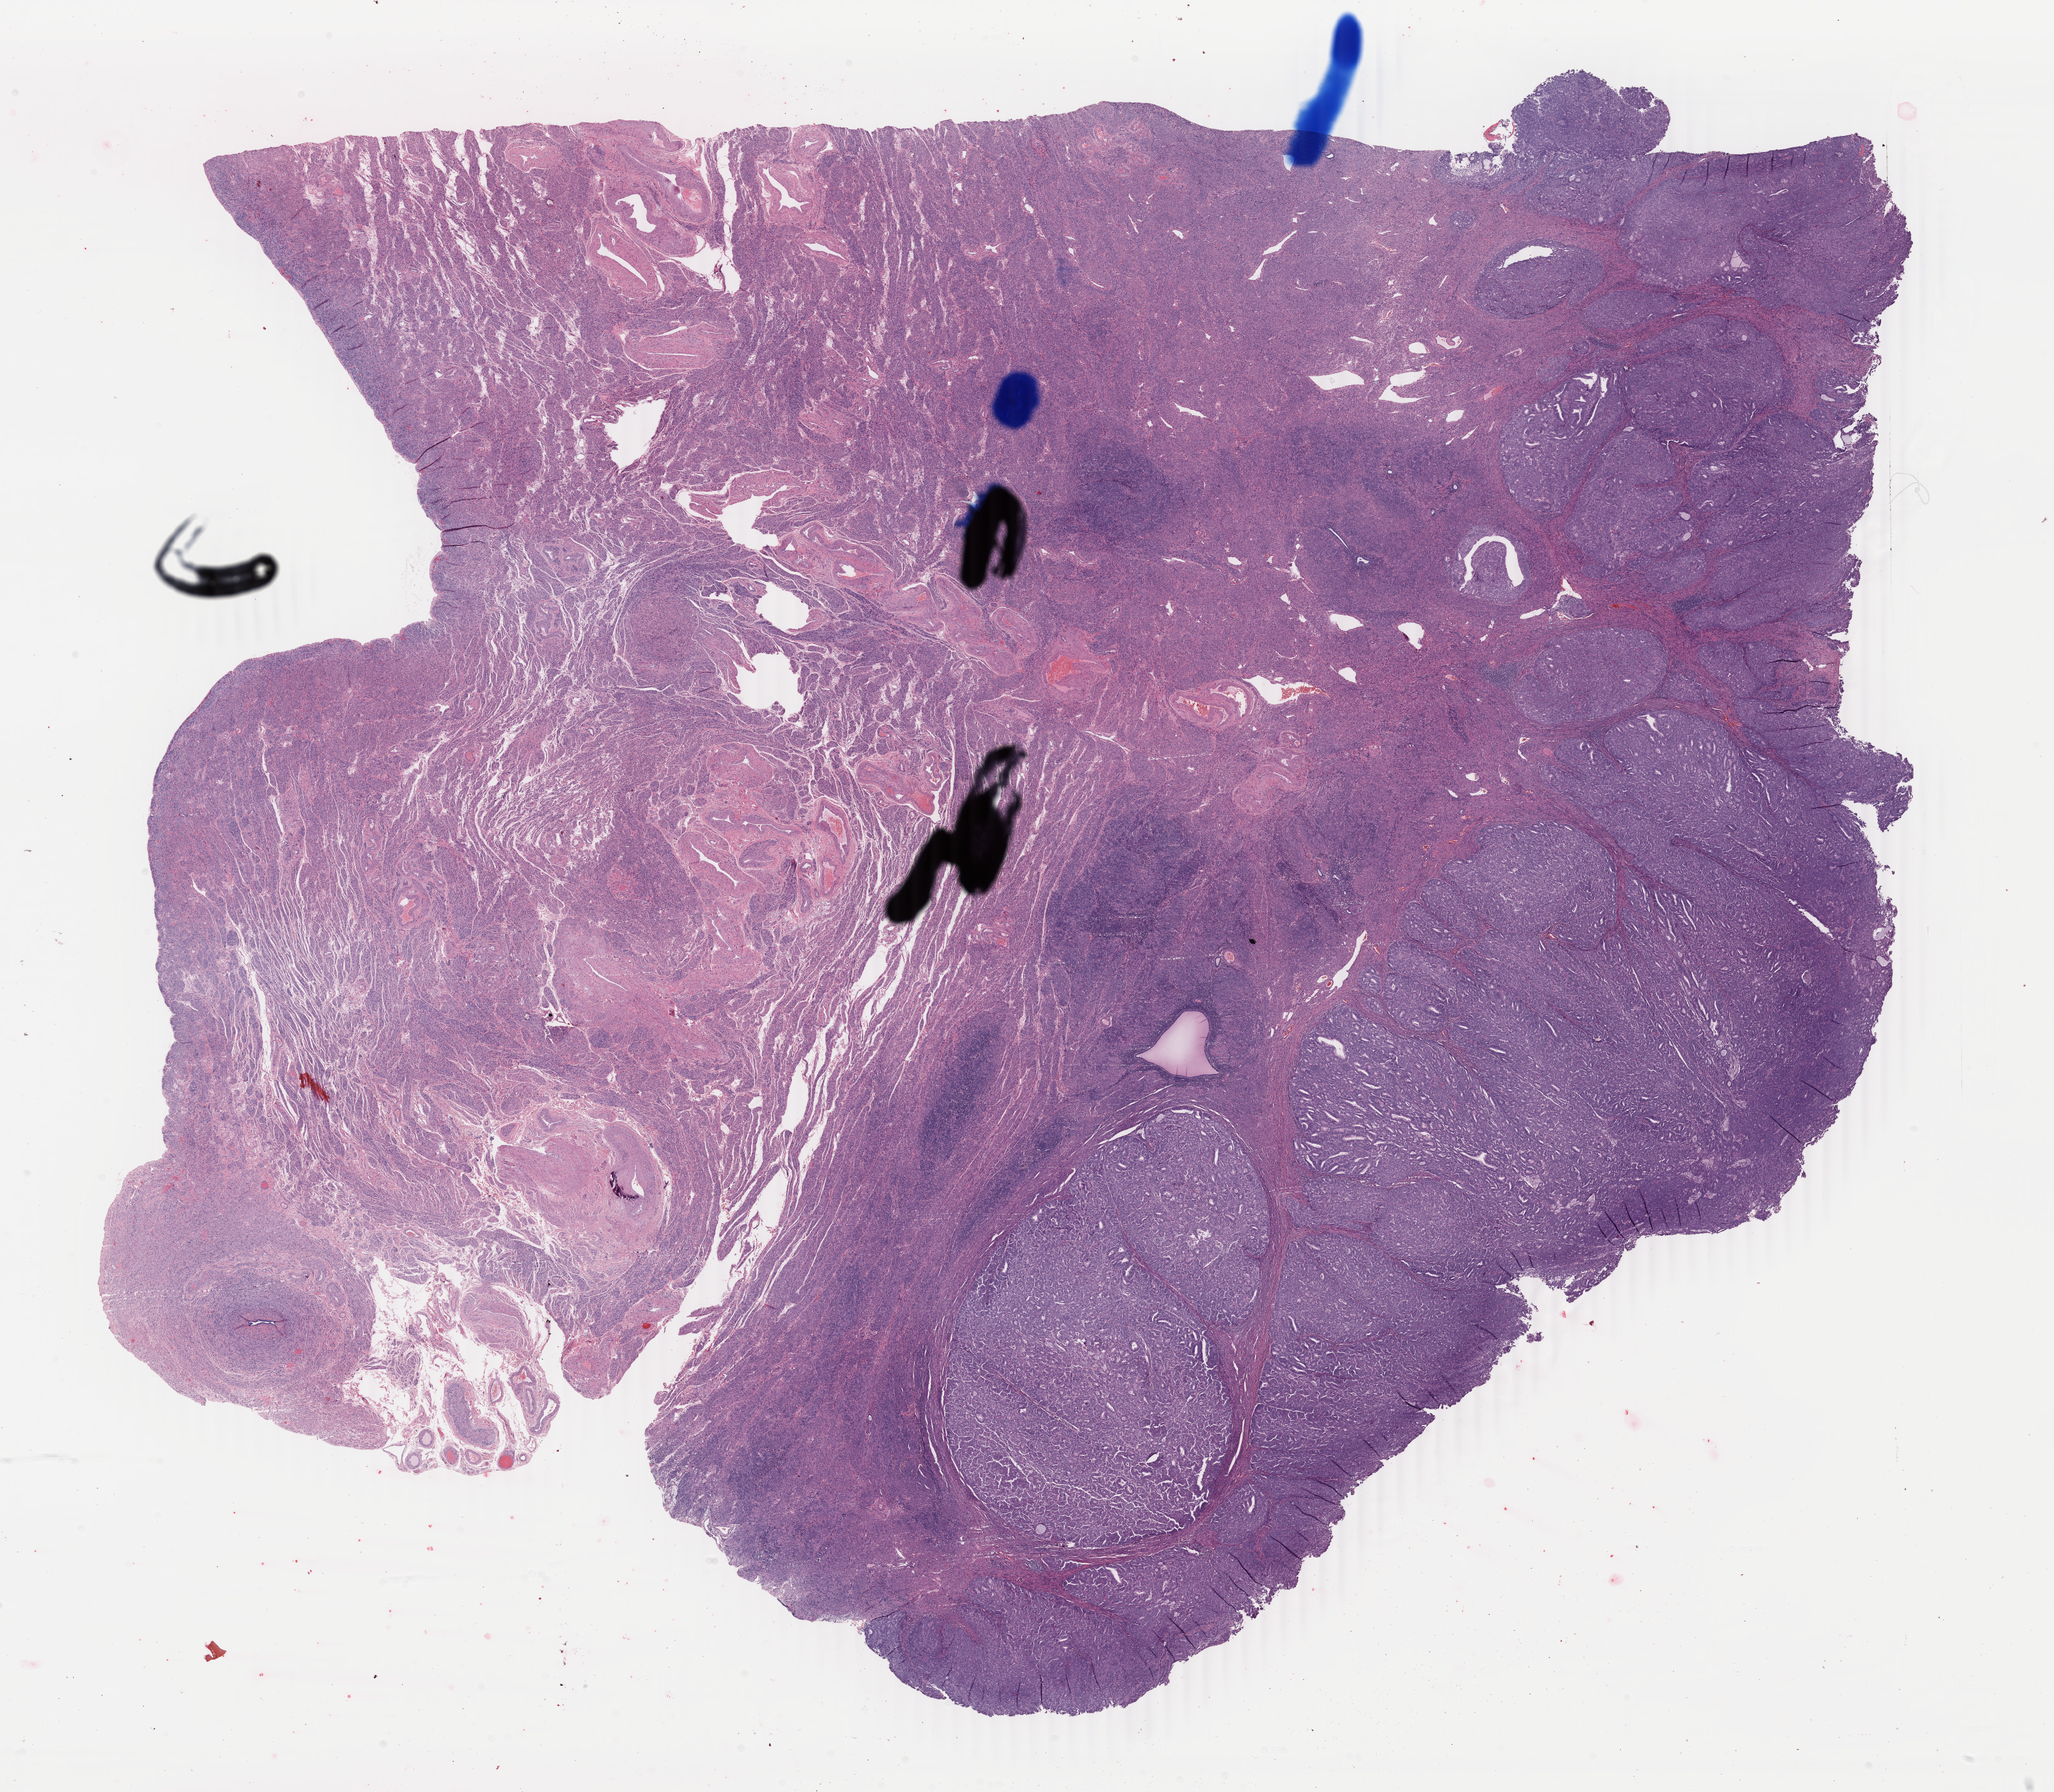
Digitized Hematoxylin and eosin (H&E) stained tissue section (whole slide), low-resolution overview of the scanned area, about 25.2 x 22.0 mm; FFPE section; sample: primary tumour, uterus. Patient sex: female. Histologic grade: G2 (moderately differentiated).
FIGO stage: II. Diagnosis: Endometrioid adenocarcinoma, NOS (endometrium).